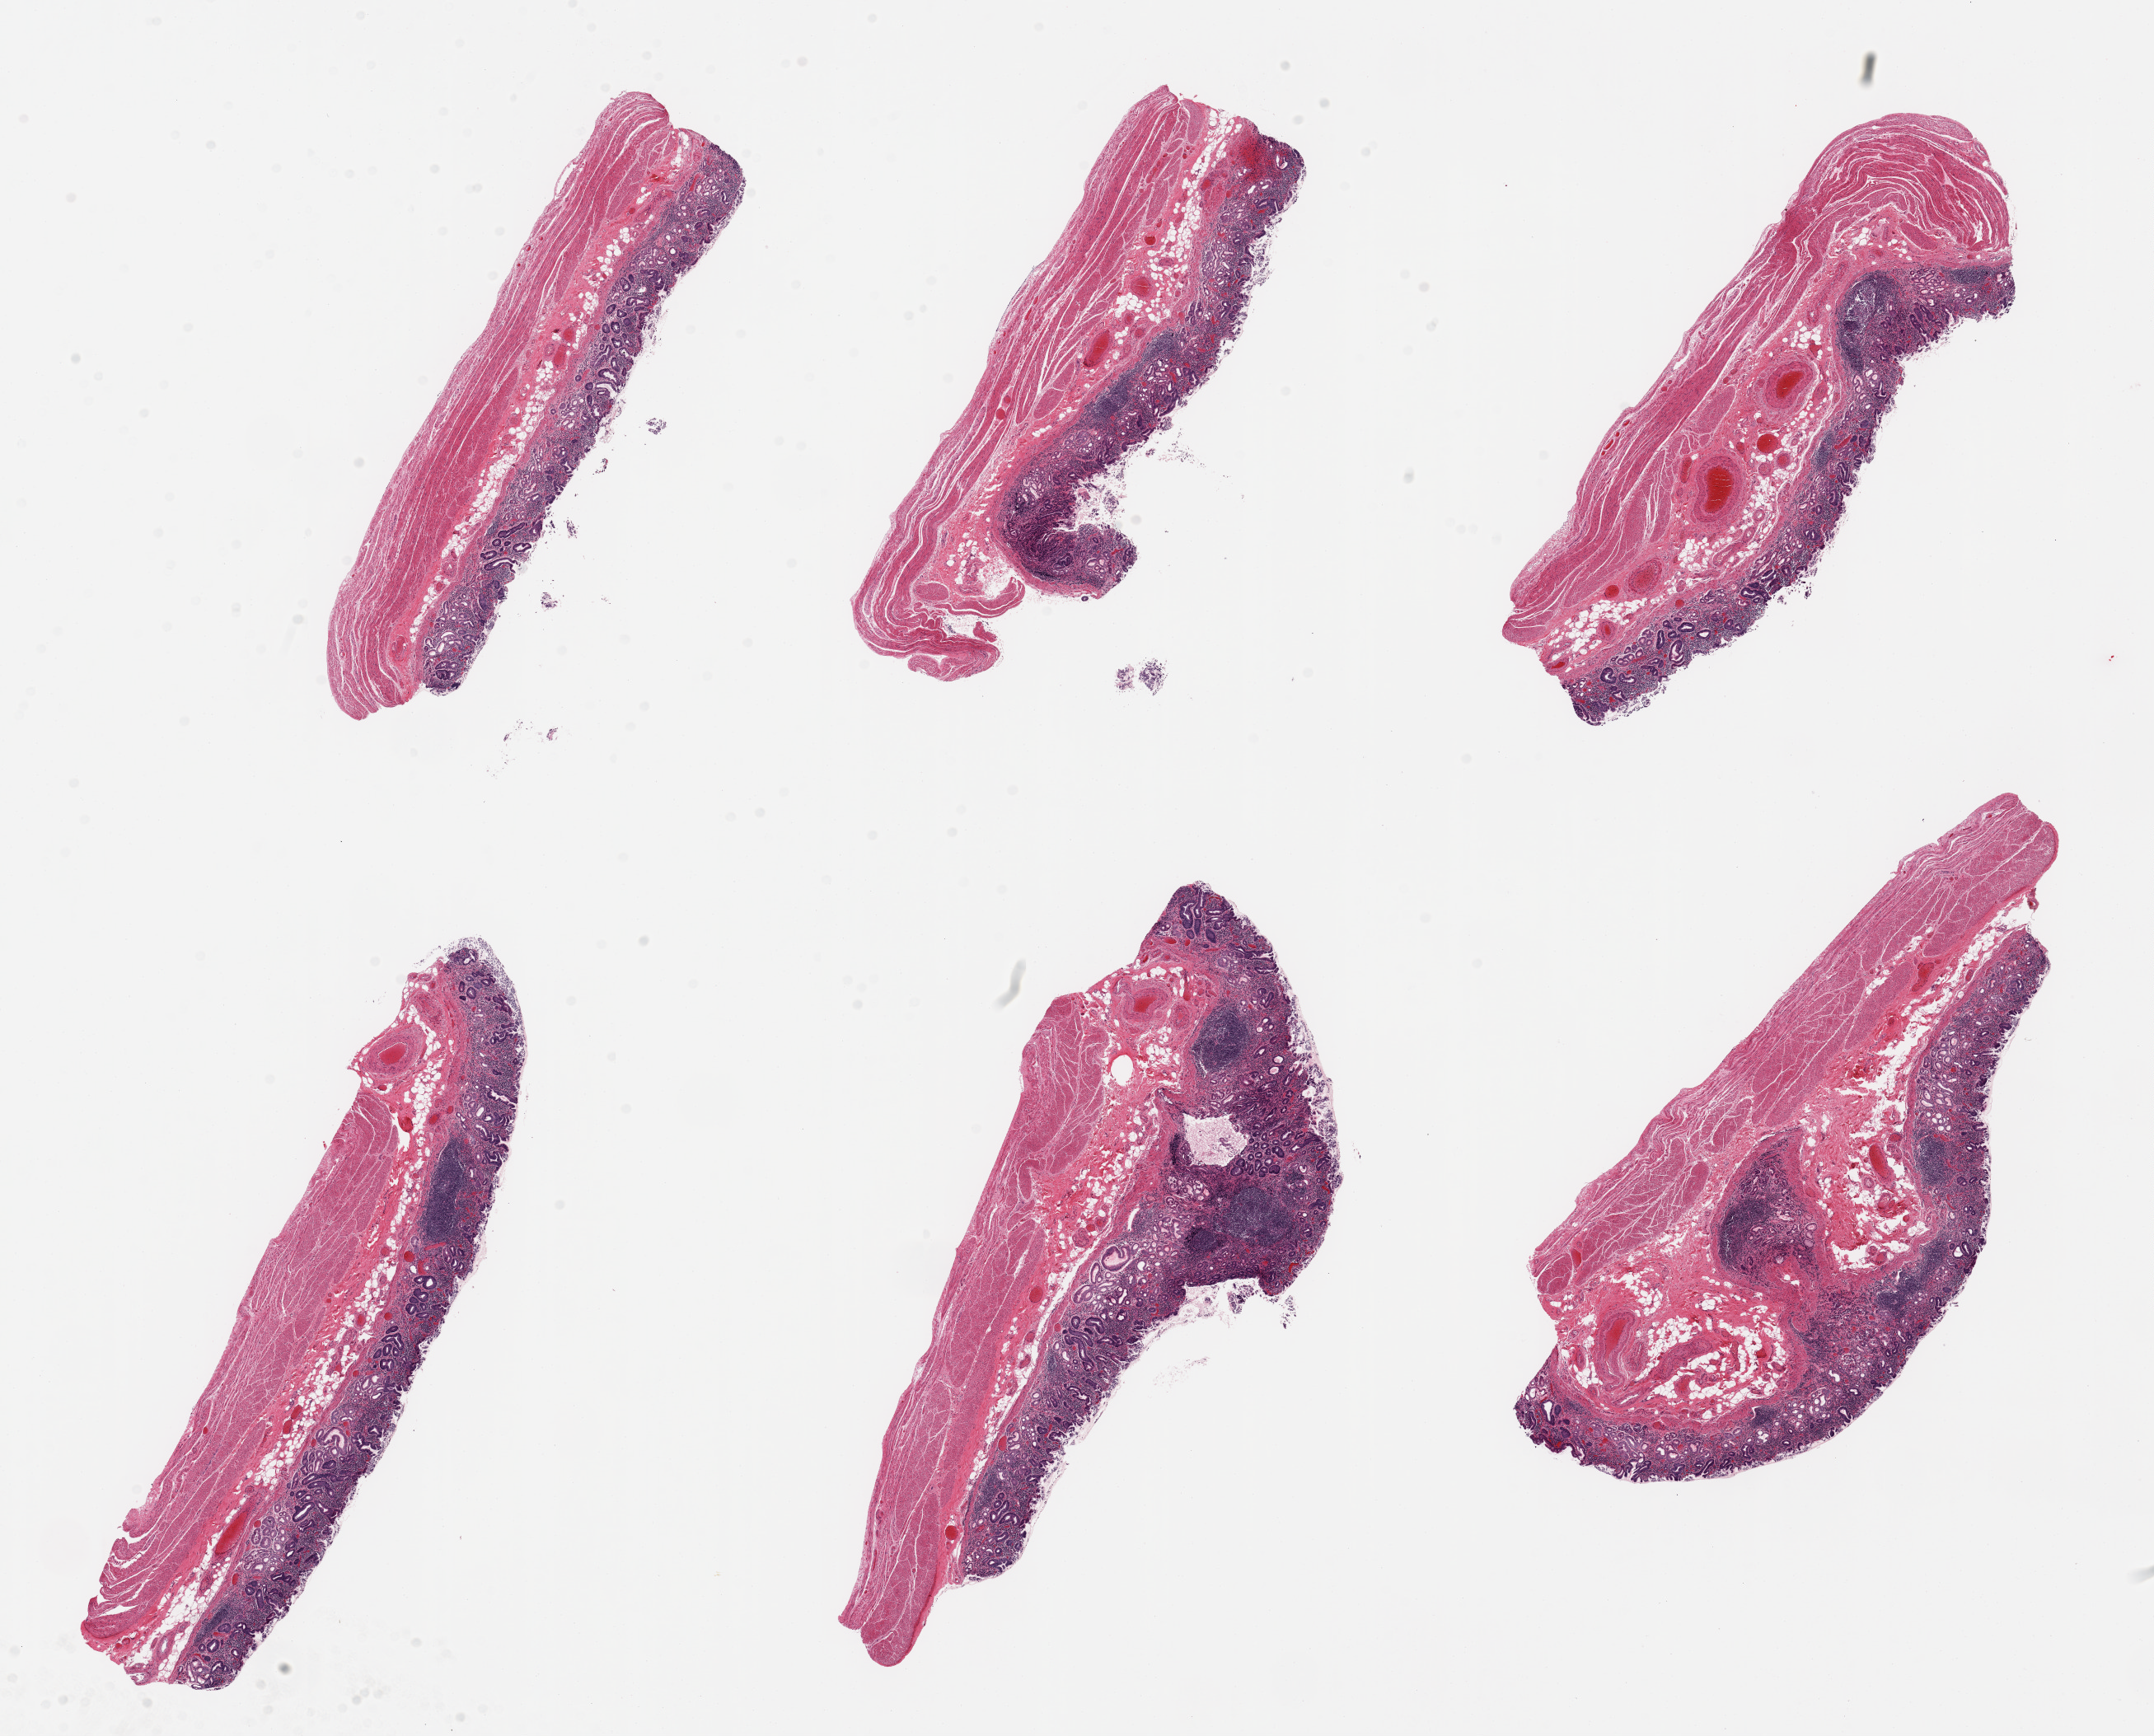
Whole-slide image, haematoxylin and eosin stain — low-resolution overview of the scanned area, about 20.7 x 16.7 mm; PAXgene-fixed, paraffin-embedded tissue; section of stomach (target tissue); tissue donor sample. Donor sex: female.
Review note (as recorded): 6 pieces; chronic atrophic gastritis with 60% reduction of gastric glands and replacement by chronic inflammatory cells; mucosa not useable, but other layers intact and without lesions.